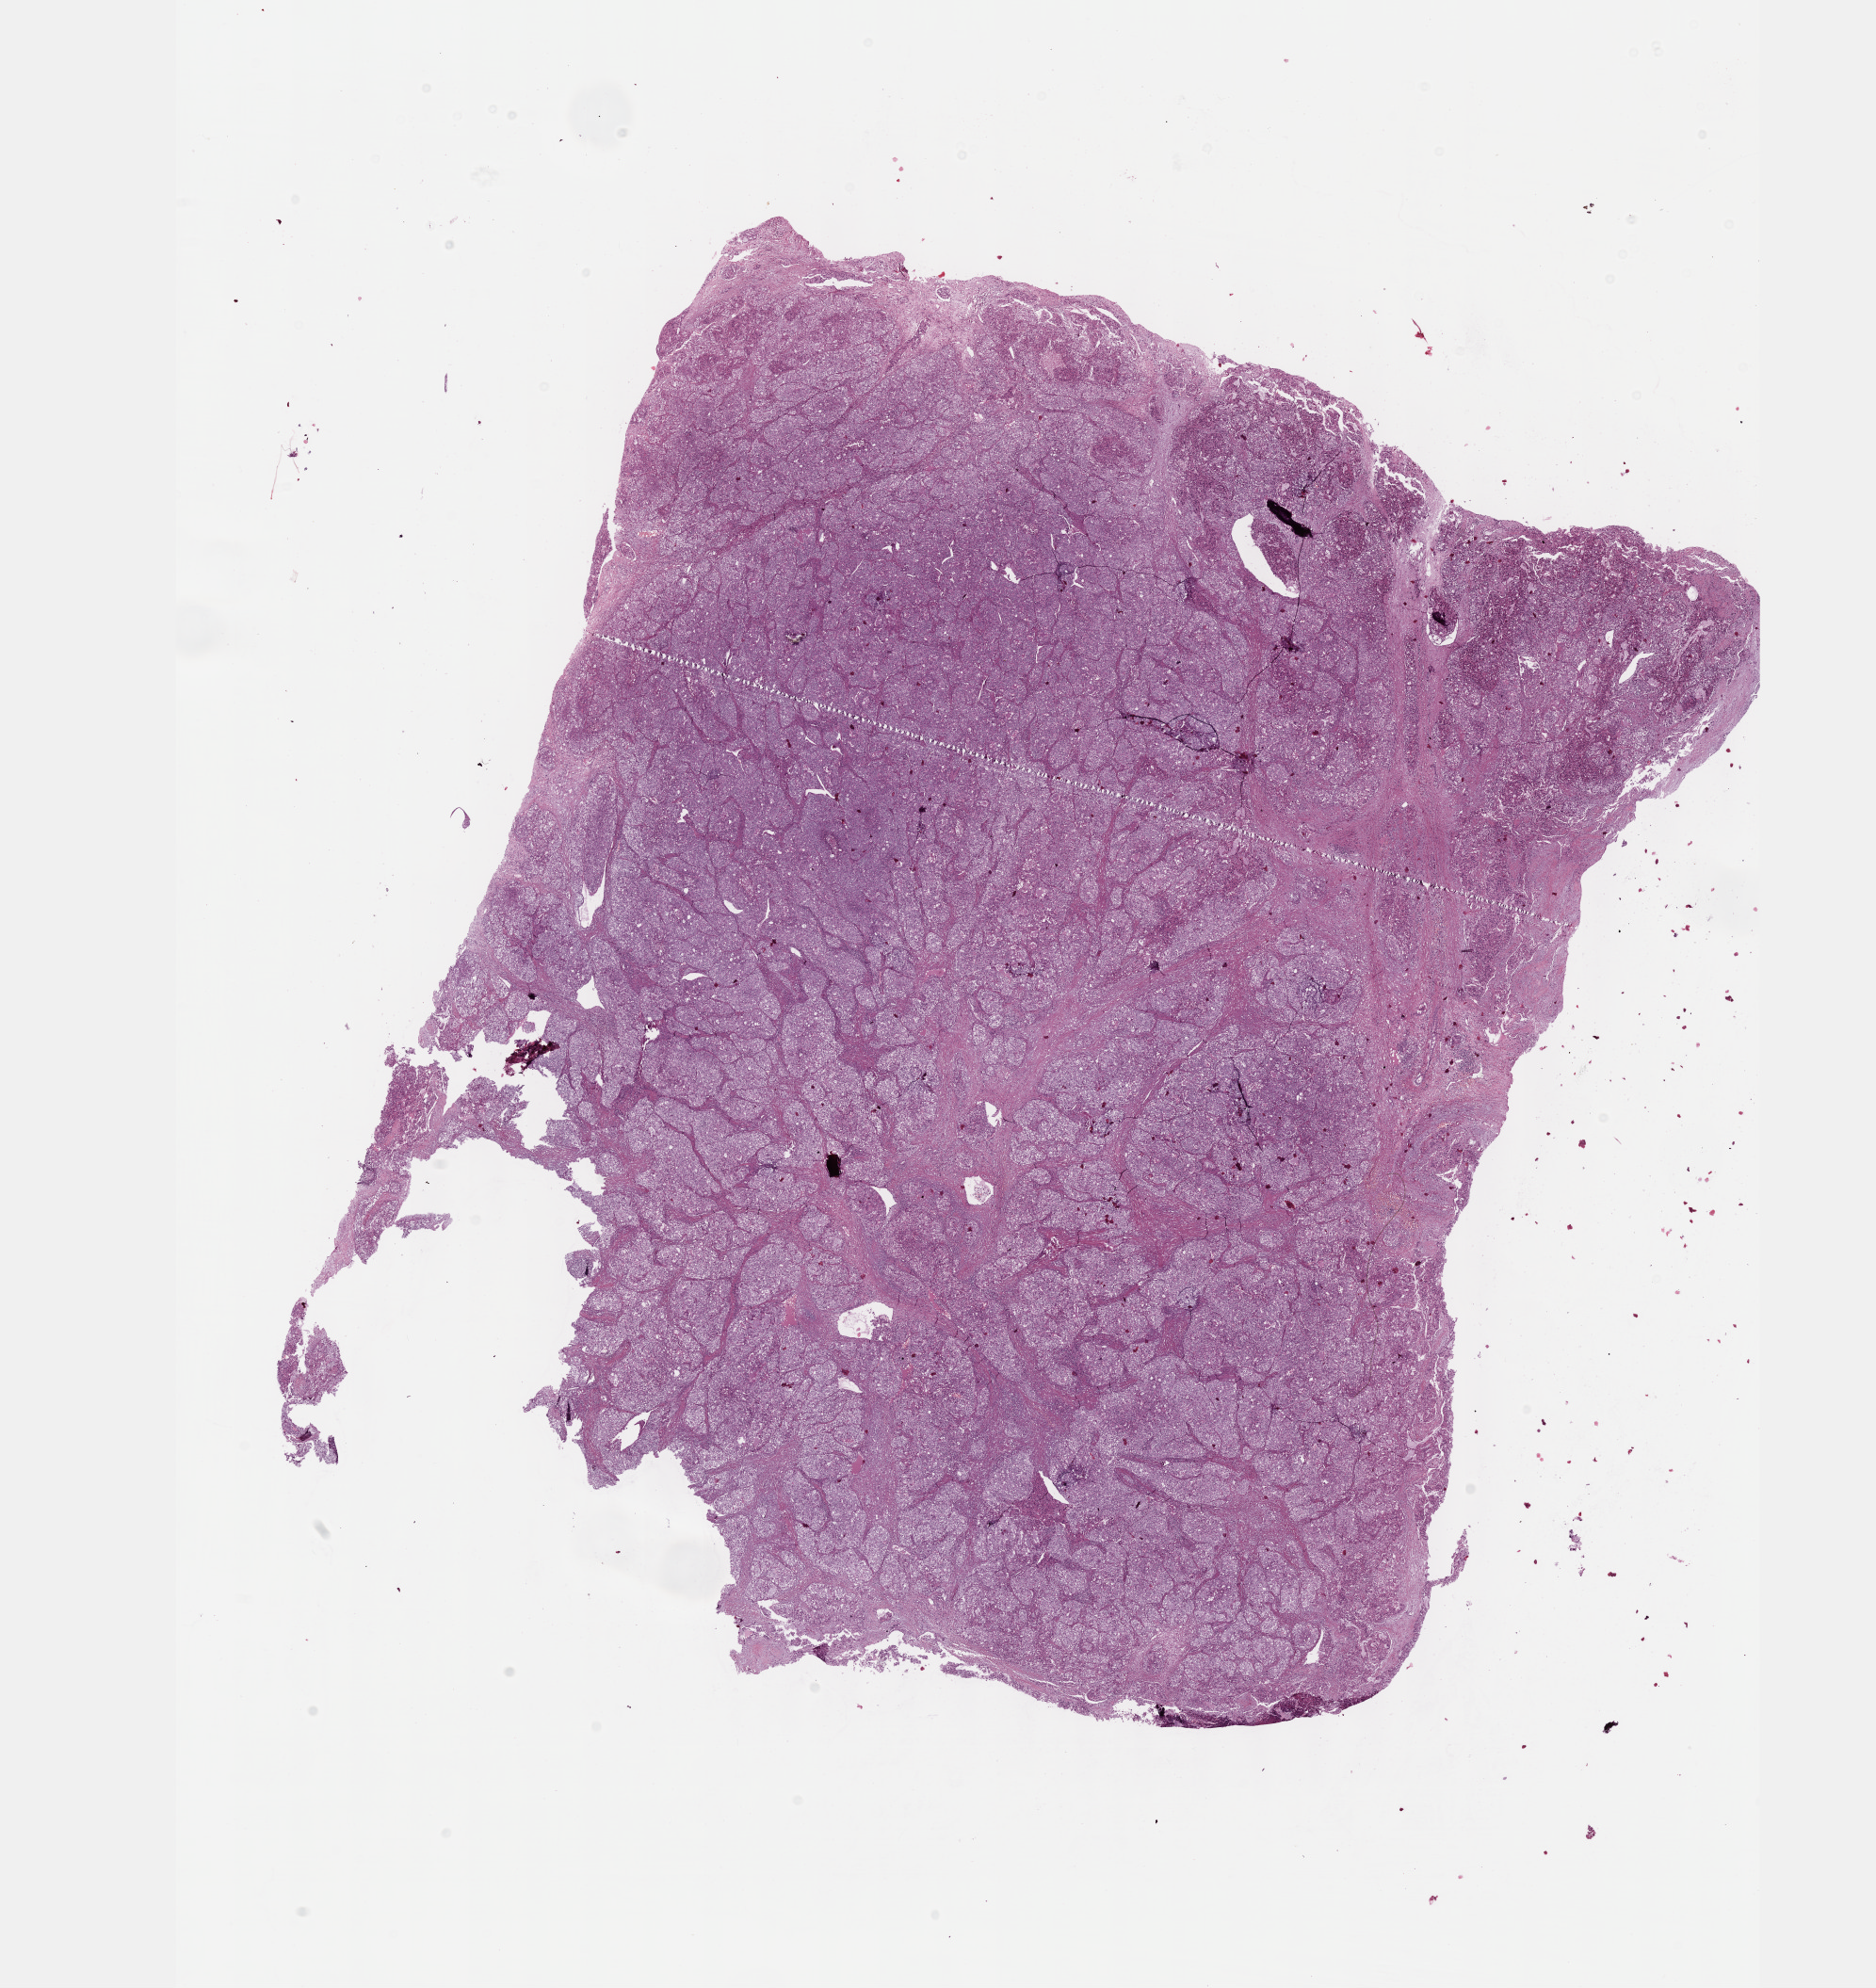
Whole-slide histology image, Hematoxylin and eosin (H&E) stained, a low-resolution overview of the entire scanned area, about 16.1 x 17.1 mm (slide scanned at 40x). FFPE section. Sample: primary tumour, liver. Female patient; age at initial diagnosis 51 years. Histologic grade: G2 (moderately differentiated).
AJCC pathologic stage: II (6th edition). TNM: T2 N0 M0. Histologic diagnosis: Hepatocellular carcinoma, NOS.